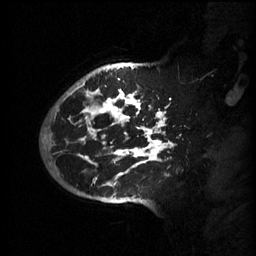
Breast MRI (dynamic contrast-enhanced), one sagittal slice. Slice 46 of 60 in the series (ordered by position). 3 images stored at this slice position (order not interpretable as contrast timing). 1.5 T. TE 4.2 ms, TR 11 ms. 256 × 256 image matrix, field of view 220 × 220 mm. Patient: female, 51 years.
Annotated regions visible in this slice (semi-automatically segmented with operator editing):
- analysis volume of interest (the breast-tissue region the enhancement analysis was run in; not a lesion): bounding box (x1, y1, x2, y2) in pixels: (63, 80, 182, 201)
- tumour enhancement mask (voxels above the 70 % enhancement threshold inside the analysis volume of interest): (64, 80, 174, 187)